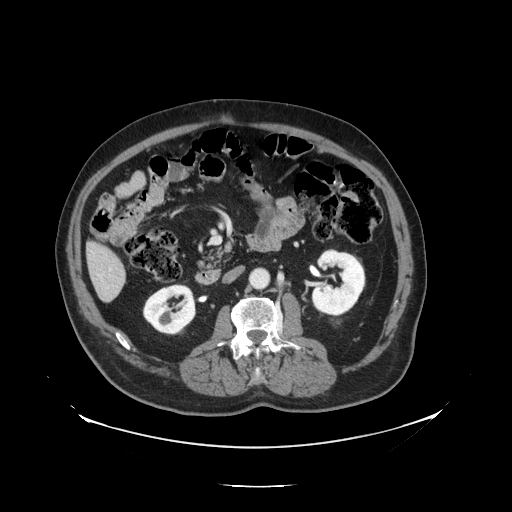
Contrast-enhanced abdominal CT, one axial slice; slice 43 of 138 in the series (ordered by position); 120 kVp; intravenous contrast given; soft-tissue window (W 400 / L 40 HU); 2.5 mm slice thickness; 512 × 512 image matrix, field of view 497 × 497 mm. Male patient, age 77 years. From the clinical record (not read from this slice): diagnosis: colorectal cancer liver metastases, imaged before liver resection; multiple liver metastases: no.
Outlined on this slice (outlined manually by an expert reader):
- liver: bounding box (x1, y1, x2, y2) in pixels: (89, 244, 126, 302)
- planned liver remnant (the part of the liver to remain after resection): (88, 244, 123, 277)